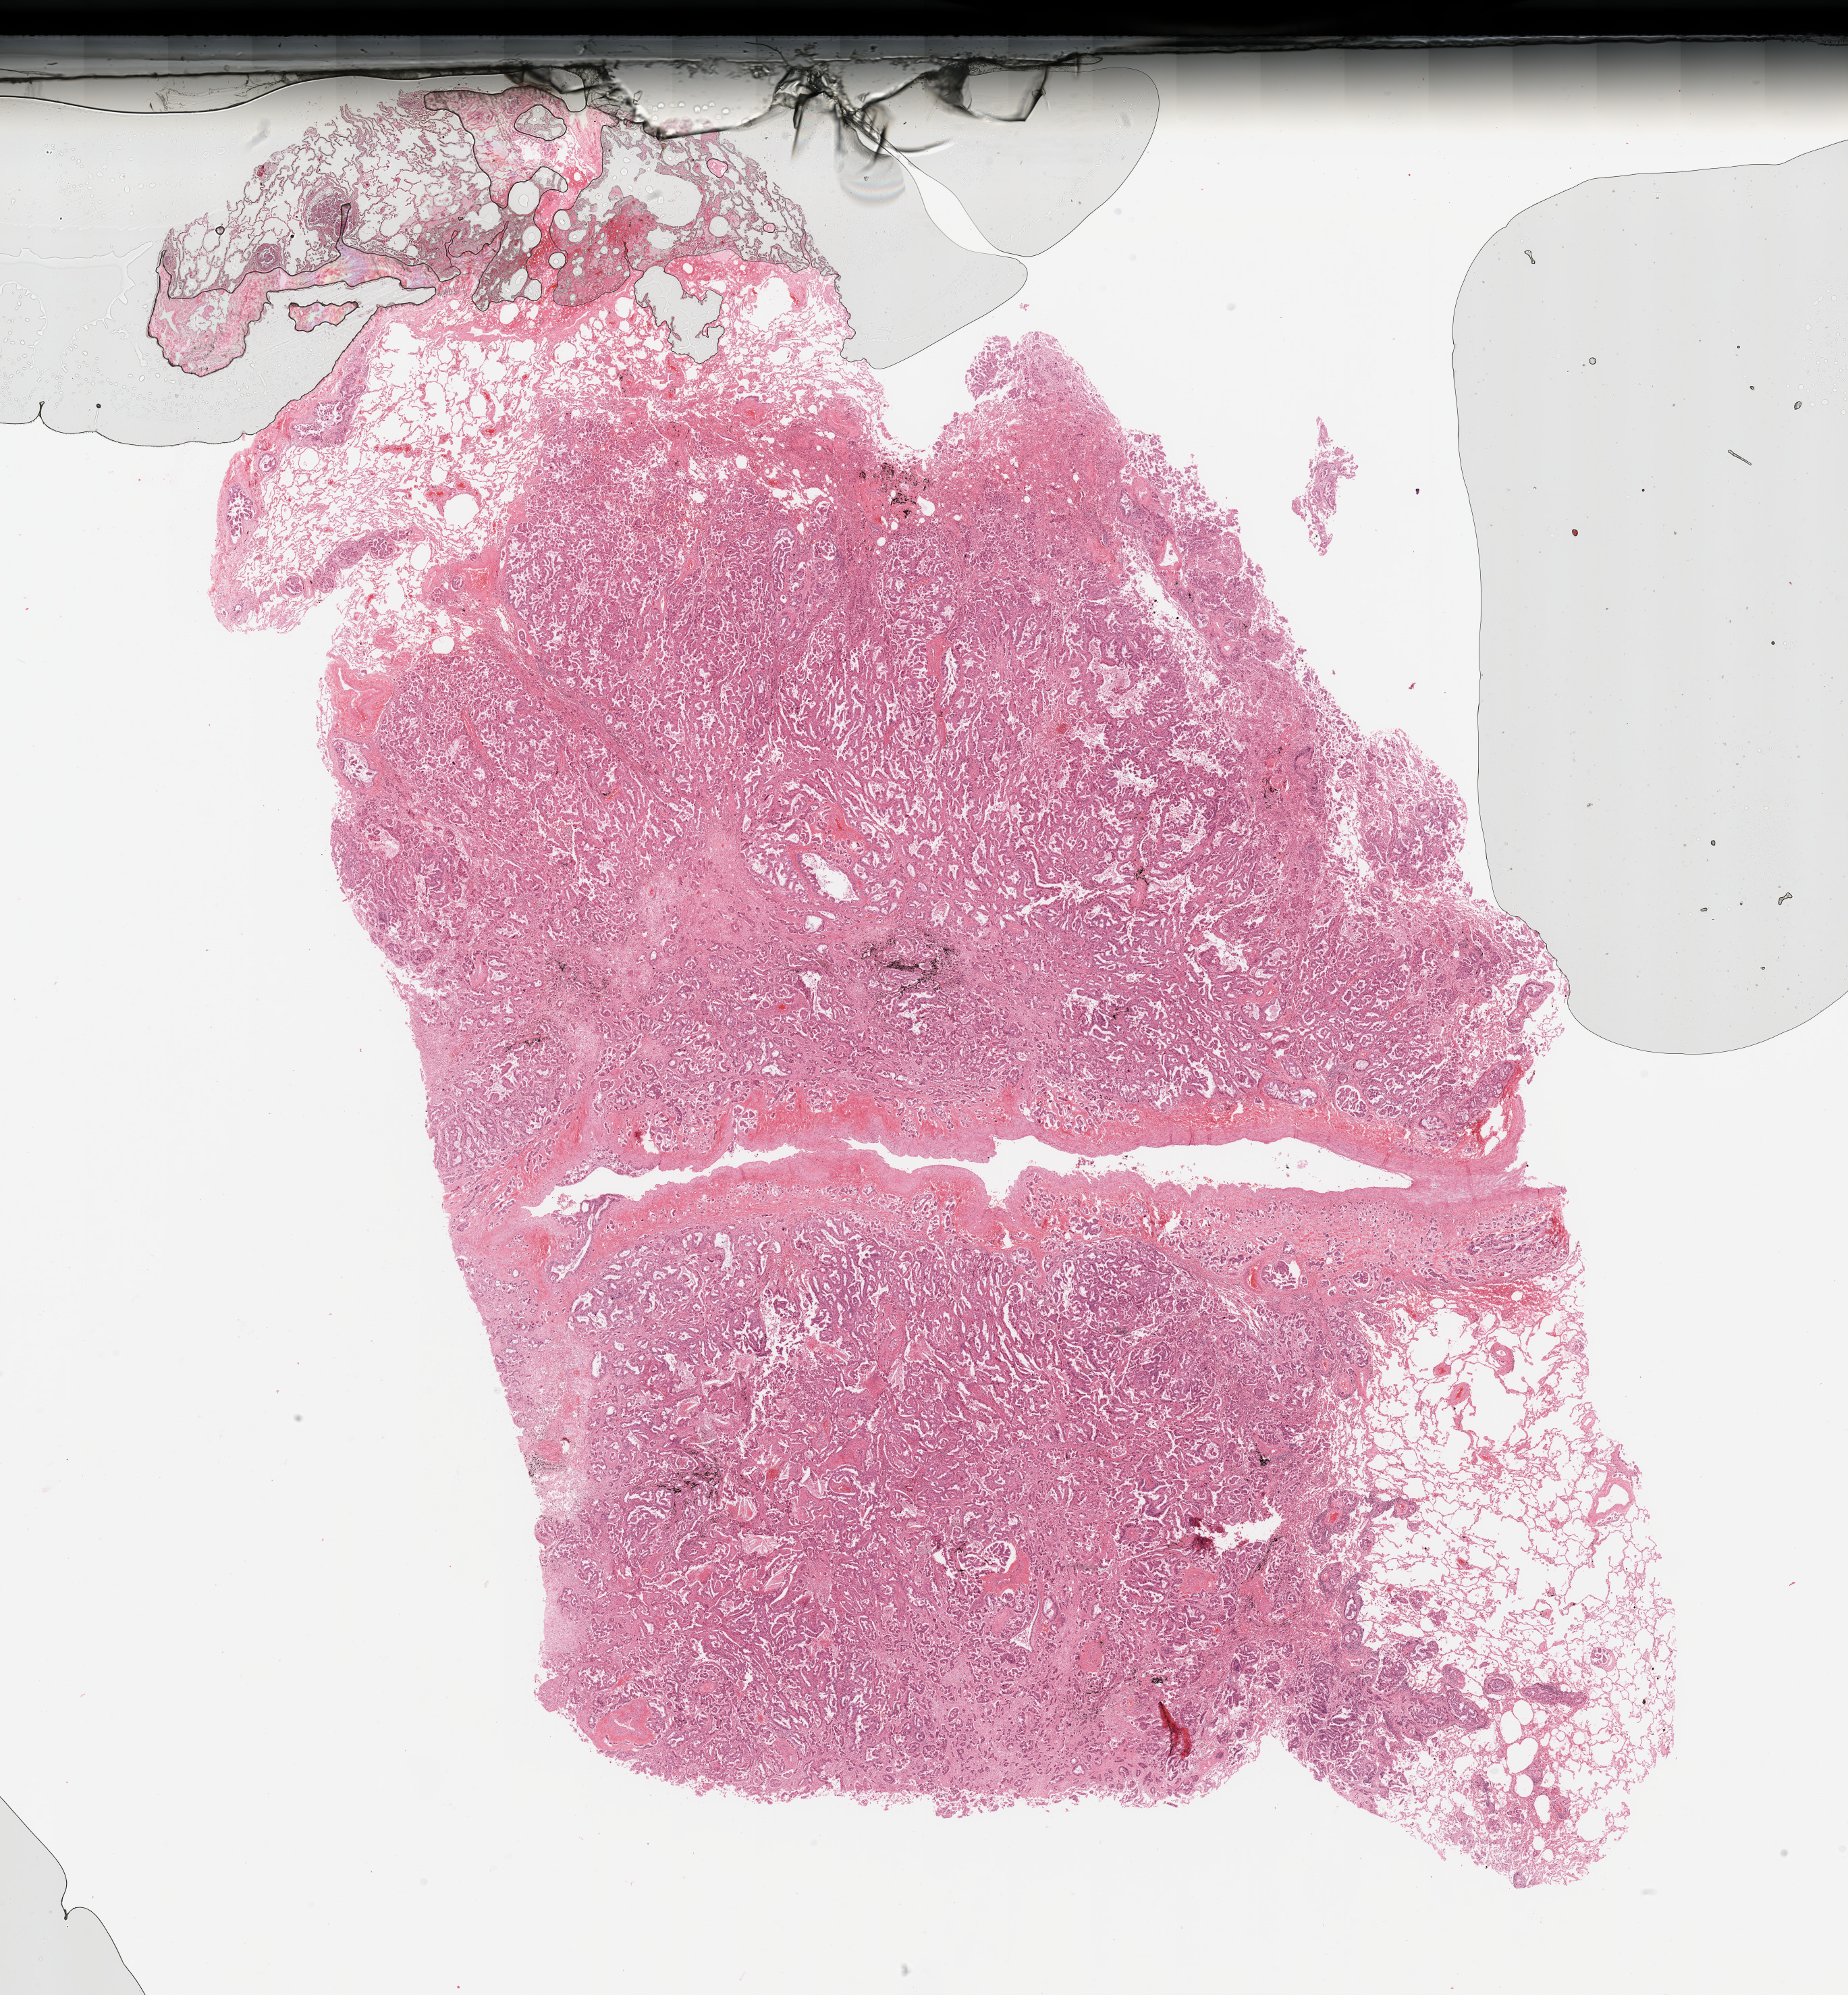
H&E whole-slide image, low-resolution overview of the scanned area, about 21.7 x 23.4 mm; tumour tissue sample, sampled site: lung. 64-year-old male patient. Histologic grade: G2 (moderately differentiated). Composition of this section per pathologist review: tumour nuclei 80%, necrosis 3%.
AJCC pathologic stage: IIA. Histologic diagnosis: Adenocarcinoma, NOS.